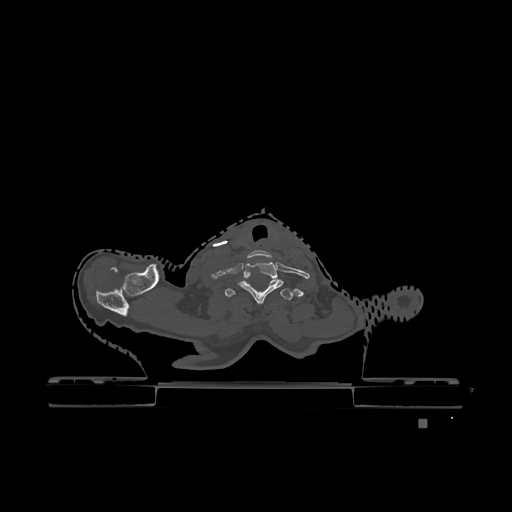
CT including the spine, one axial slice; slice 1022 of 1317 in the series (ordered by position); bone window (W 1800 / L 400 HU); 0.5 mm slice thickness; 512 × 512 image matrix, field of view 500 × 500 mm. Patient: female, 74 years. Case-level facts recorded for this patient, not image findings: primary cancer: lung; vertebrae with lytic lesions (as recorded): T1, T4, T5, T6, L4, L5.
Annotated regions visible in this slice (semi-automatically segmented with operator editing):
- T1 vertebra: bounding box [x1, y1, x2, y2] px = [225, 281, 293, 300]